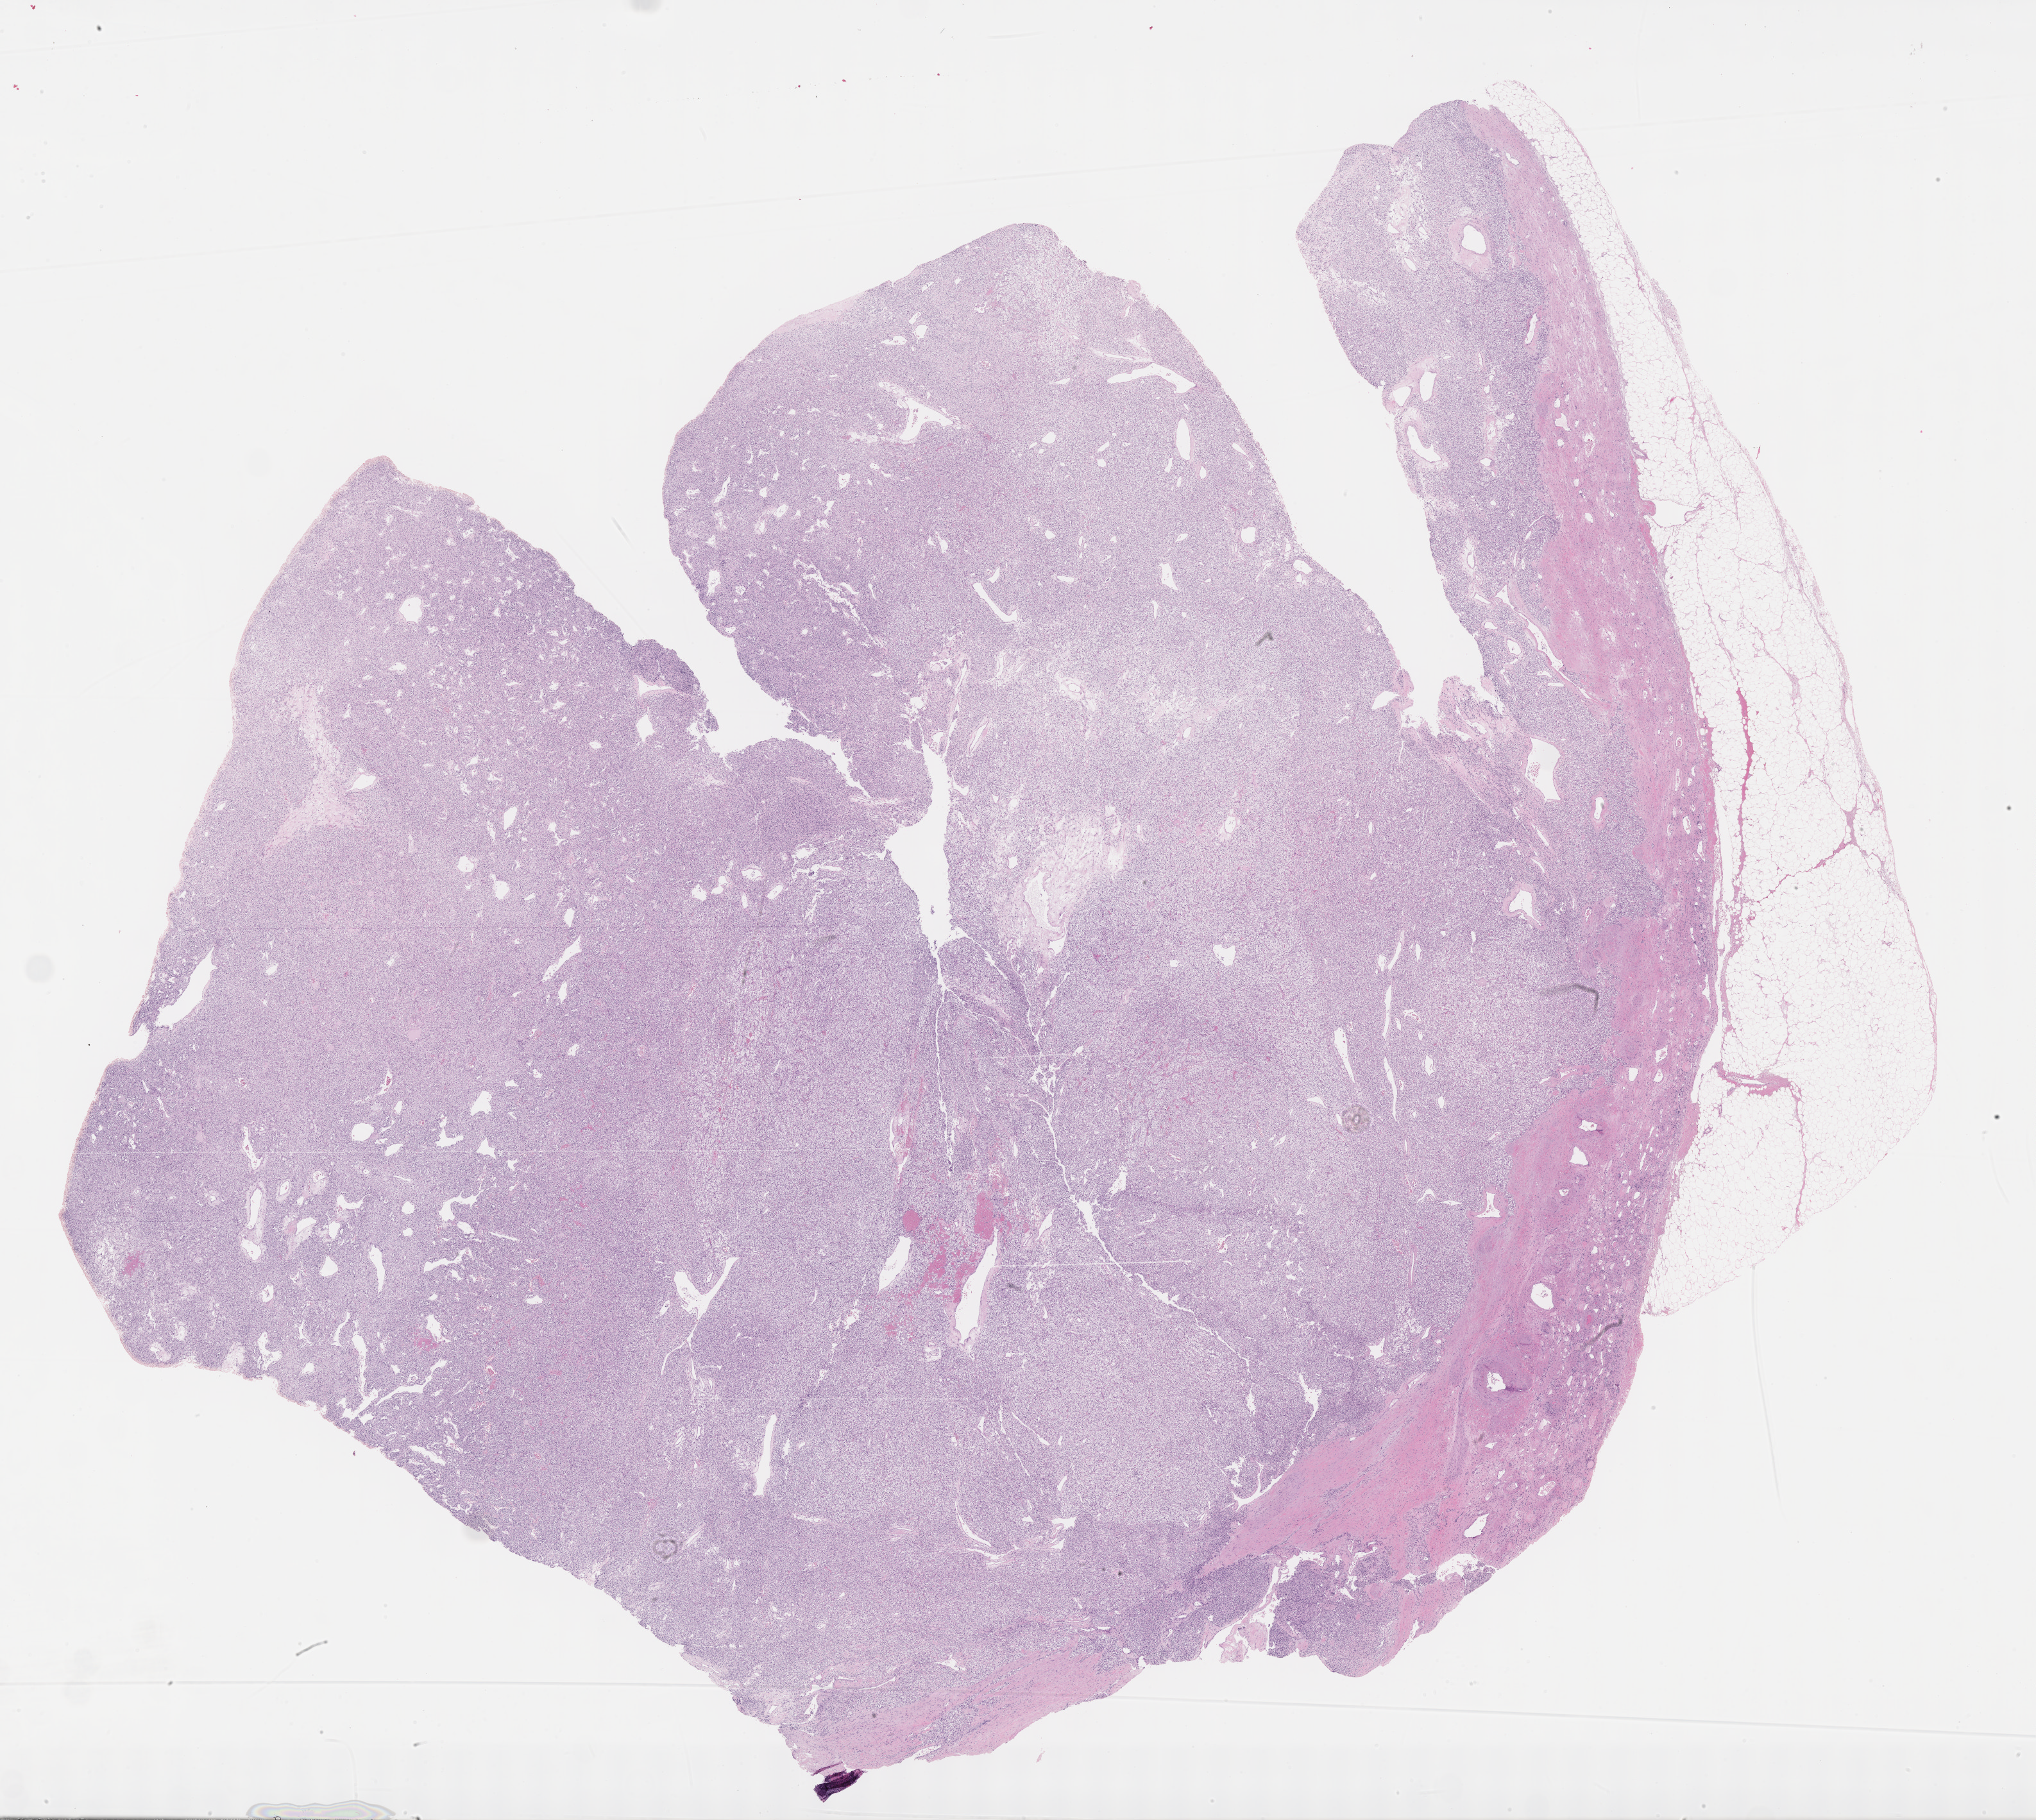
Whole-slide histology image, H&E, a low-resolution overview of the entire scanned area, about 25.7 x 22.9 mm (from a 40x scan); formalin-fixed paraffin-embedded (FFPE) diagnostic section; kidney, primary tumour sample. Patient: male, age at initial diagnosis 64 years. Histologic grade: G3 (poorly differentiated).
- TNM: T3a NX M1
- histologic diagnosis: Clear cell adenocarcinoma, NOS
- AJCC pathologic stage: IV